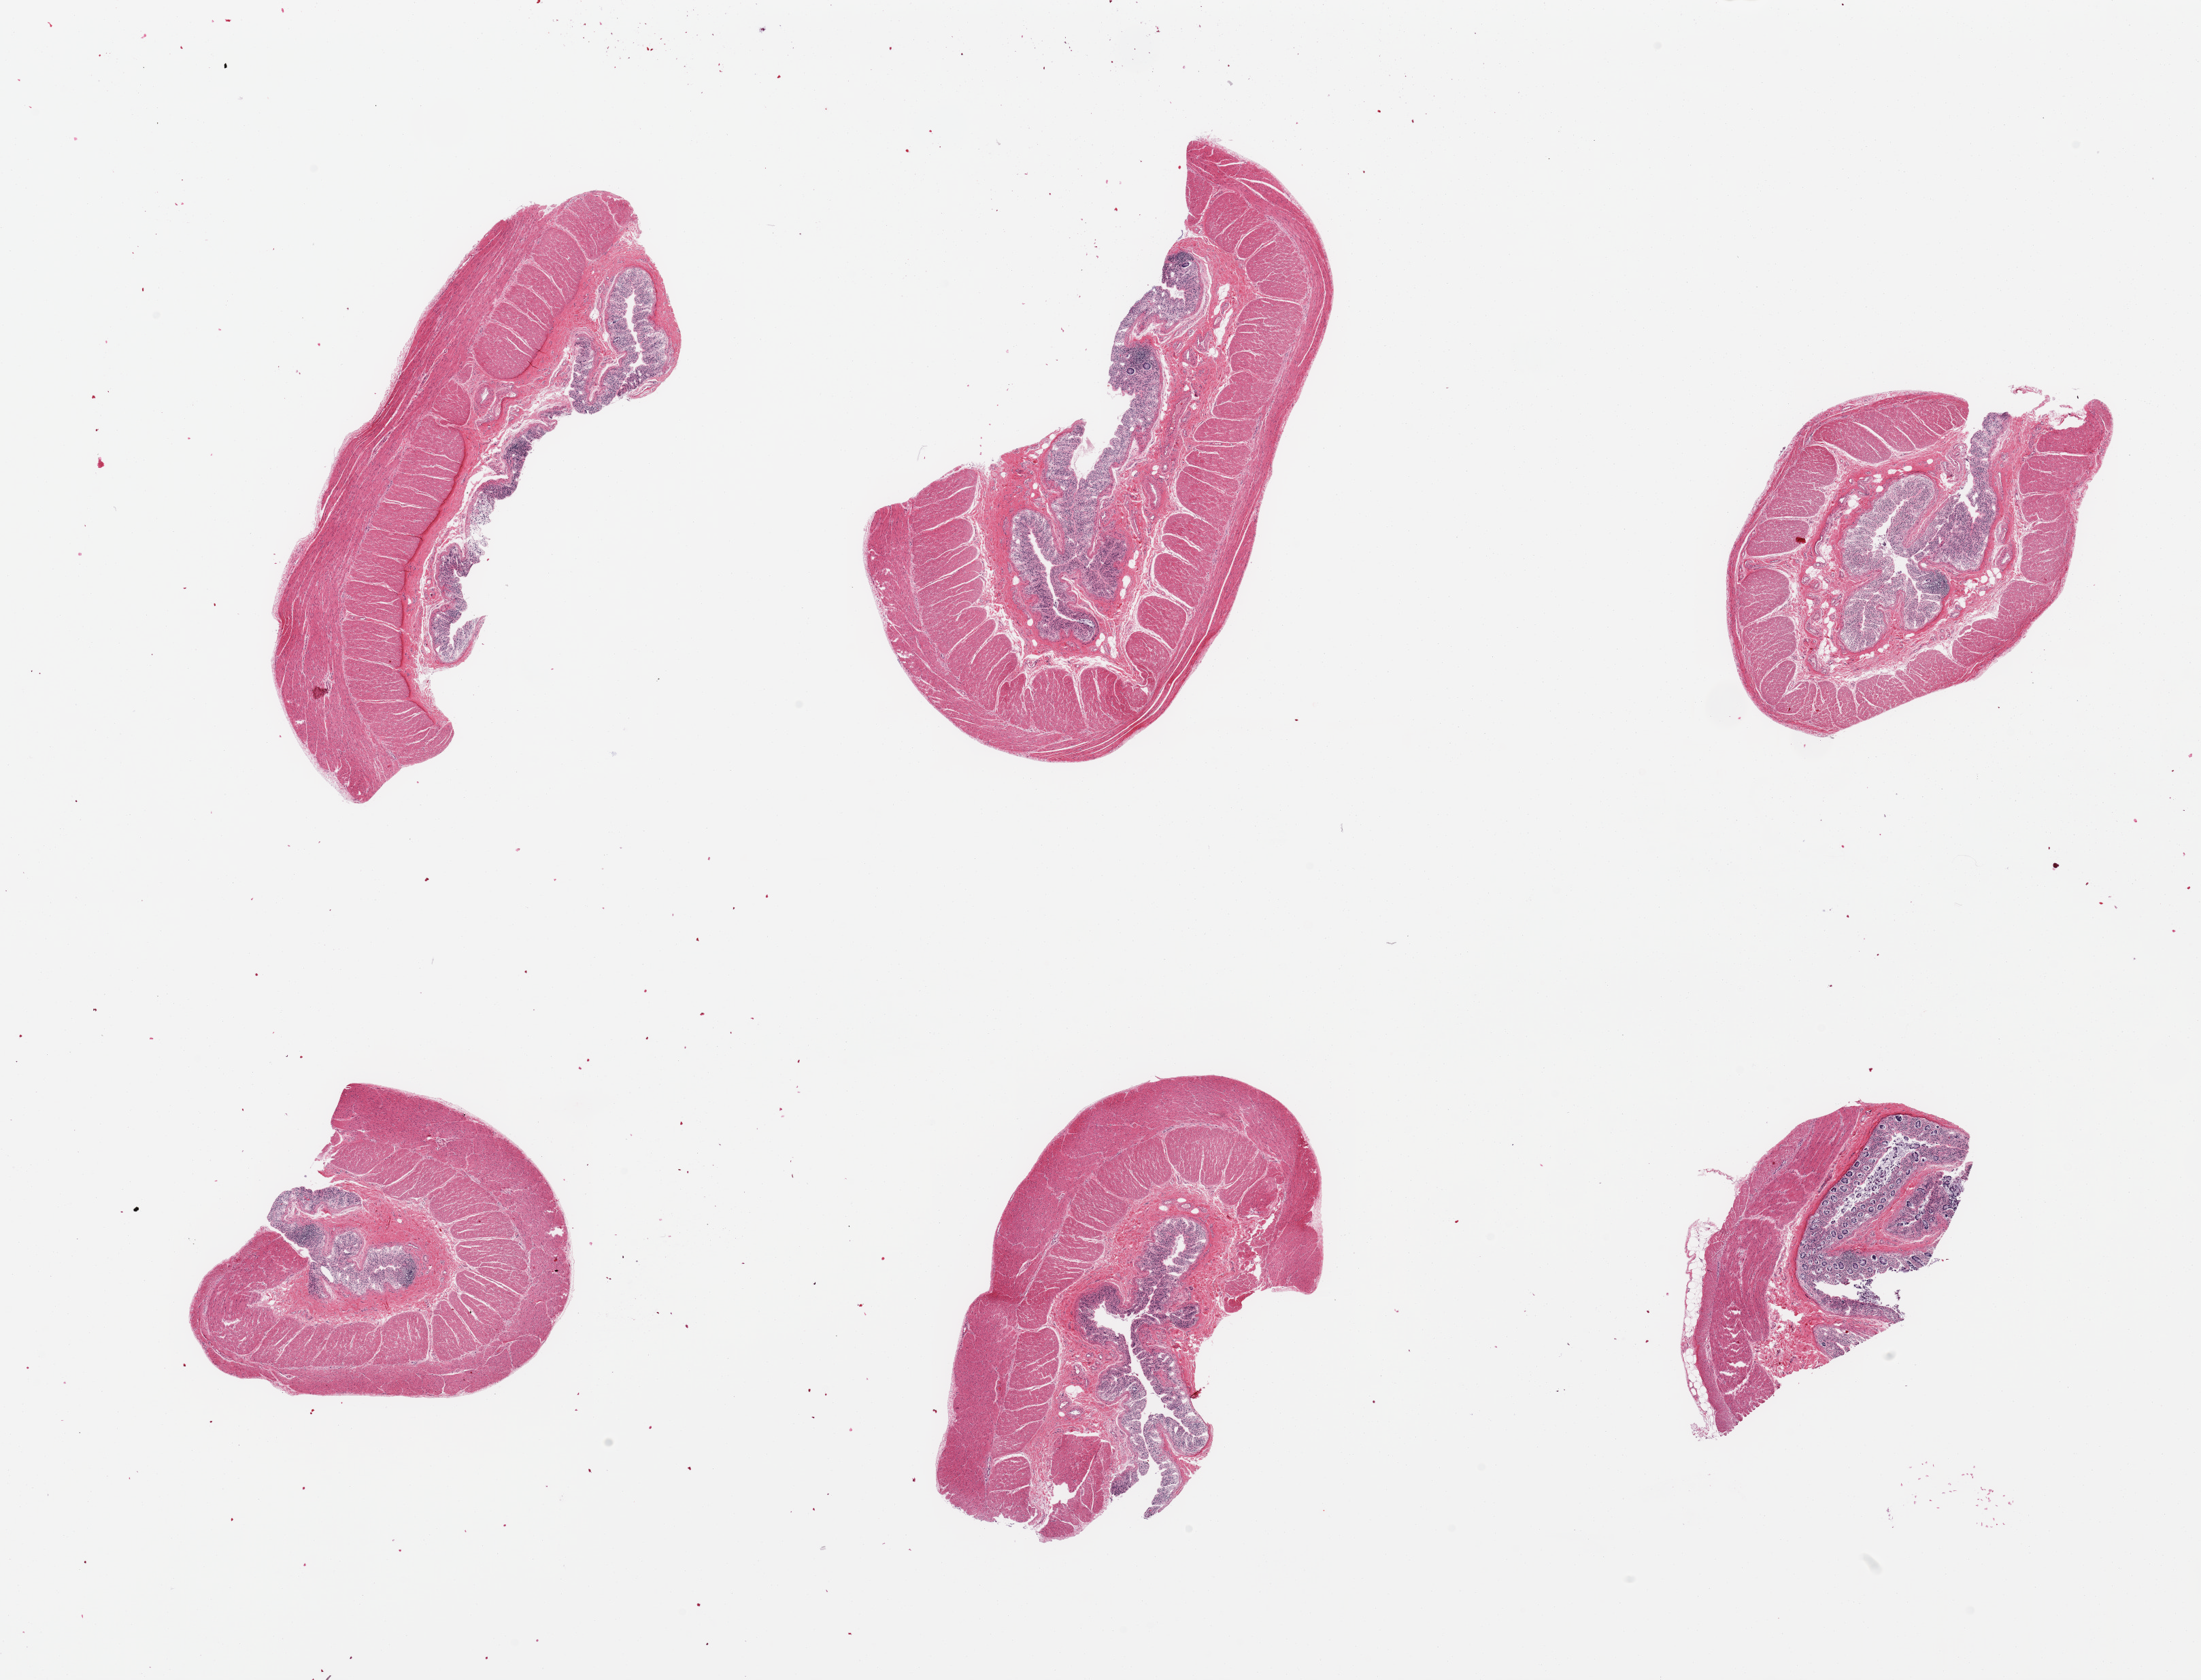
Digitized H&E-stained section, brightfield — low-resolution overview of the scanned area, about 25.6 x 19.5 mm; PAXgene-fixed paraffin-embedded (PFPE) section; target tissue: sigmoid colon; donor tissue sample. Donor: male.
Pathologist's review note for this sample: 6 pieces; full thickness sampled.